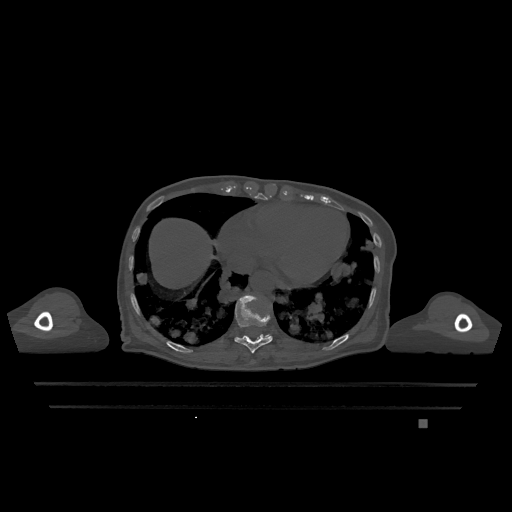
CT including the spine, one axial slice. Position 632 of 1317 along the scan axis. Bone window (W 1800 / L 400 HU). 512 × 512 image matrix, field of view 500 × 500 mm. Patient: female, 74 years. Case-level facts recorded for this patient, not image findings: primary cancer: lung; vertebrae with lytic lesions (as recorded): T1, T4, T5, T6, L4, L5.
Outlined on this slice (semi-automatically segmented with operator editing):
- T10 vertebra: bounding box <234,294,273,353> (left, top, right, bottom; pixels)